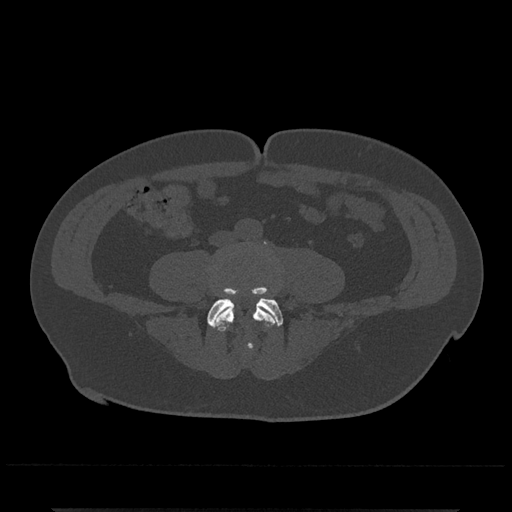
CT including the spine, one axial slice. Position 119 of 797 along the scan axis. 120 kVp. Bone window (W 1800 / L 400 HU). 0.5 mm slice thickness. 512 × 512 image matrix, field of view 393 × 393 mm. Male patient, age 67 years. From the clinical record (not read from this slice): primary cancer: prostate.
Structures marked on this image (semi-automatic segmentation, software-assisted and operator-edited):
- L4 vertebra: bounding box <212,241,280,350> (left, top, right, bottom; pixels)
- L5 vertebra: <207,287,283,326>